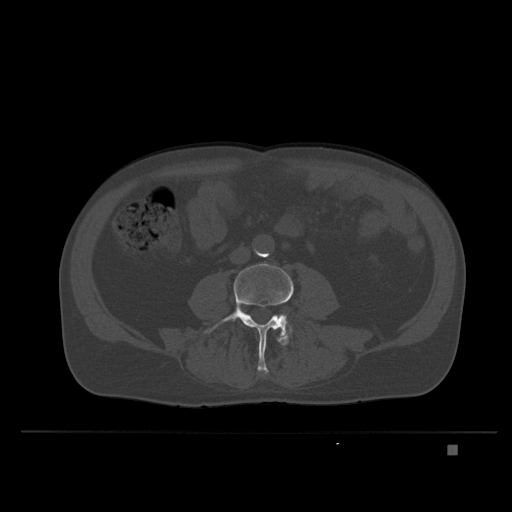
CT including the spine, one axial slice; slice 75 of 435 in the series (ordered by position); bone window (W 1800 / L 400 HU); 1.5 mm slice thickness; 512 × 512 image matrix, field of view 434 × 434 mm. Patient: male, 73 years. Case-level facts recorded for this patient, not image findings: primary cancer: skin.
Structures marked on this image (semi-automatic segmentation, software-assisted and operator-edited):
- L4 vertebra: bounding box [x1, y1, x2, y2] px = [204, 263, 294, 375]